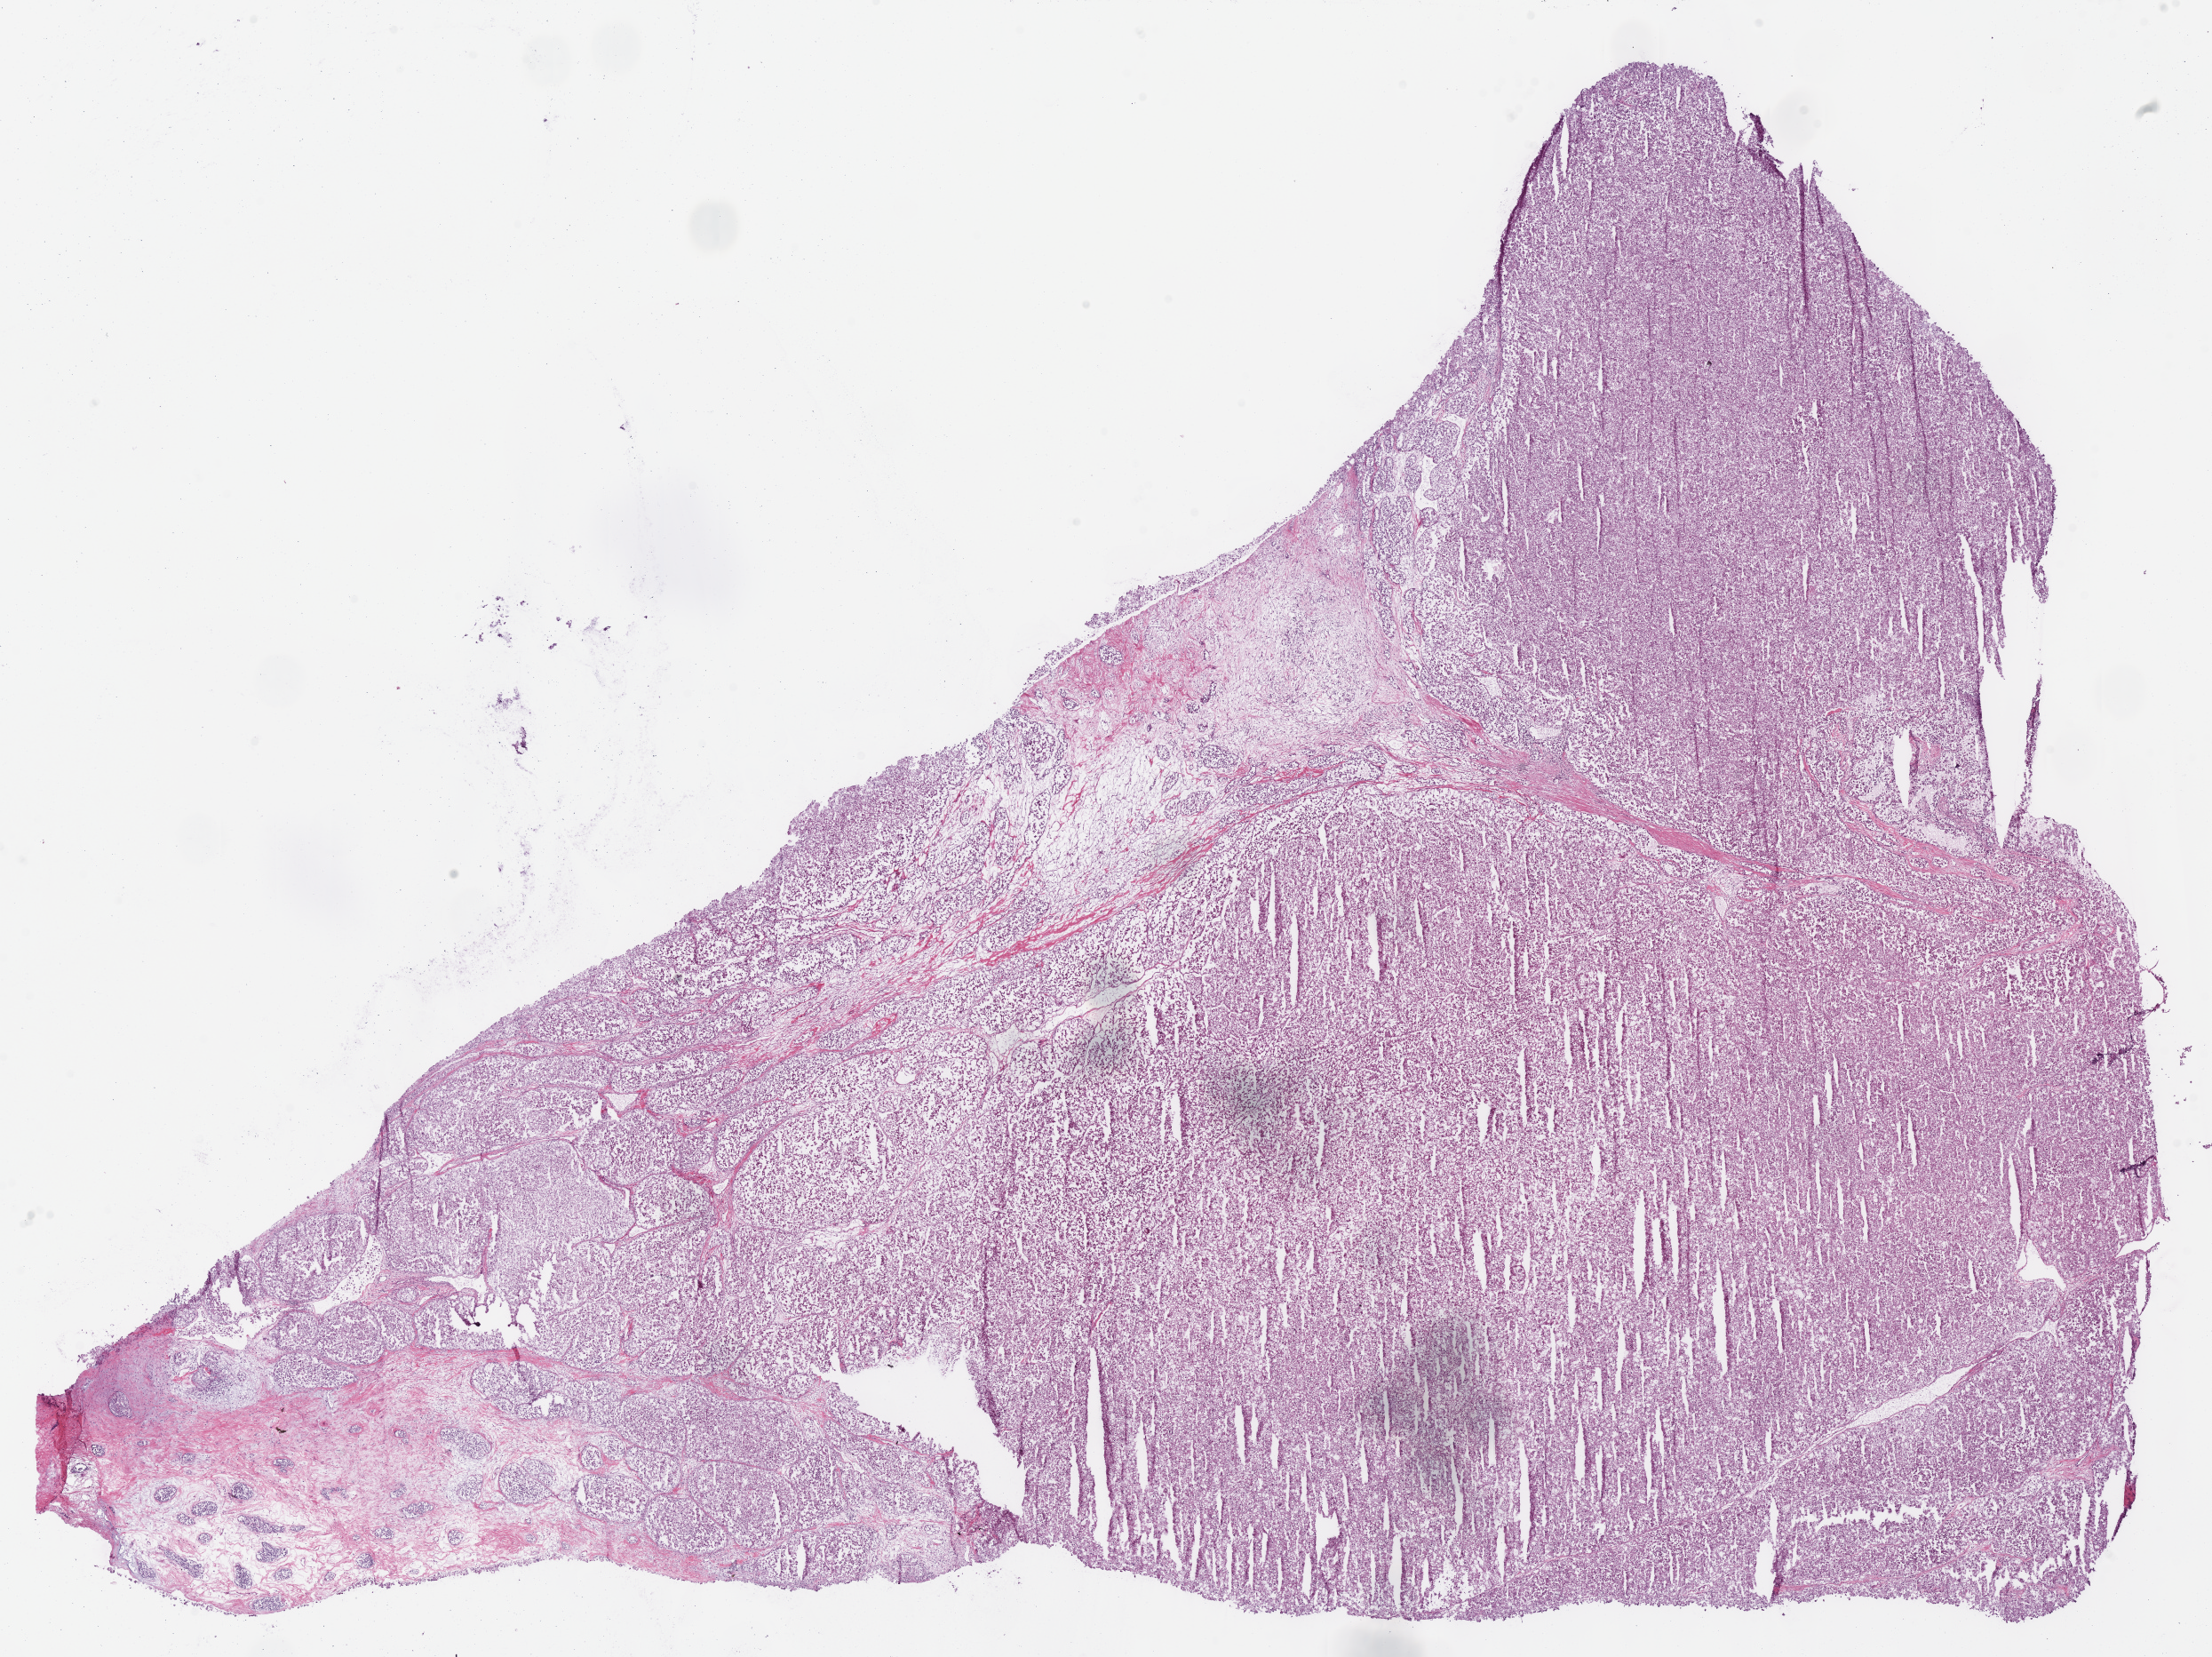
Whole-slide histology image, H&E-stained, a low-resolution overview of the entire scanned area, about 19.6 x 14.7 mm. Frozen section from the bottom of the tissue portion. Primary tumour sample from the kidney. Male, age 67 years at initial diagnosis. Composition of this section per pathologist review: tumour cells 98%, tumour nuclei 90%.
Diagnosis: Renal cell carcinoma, chromophobe type.